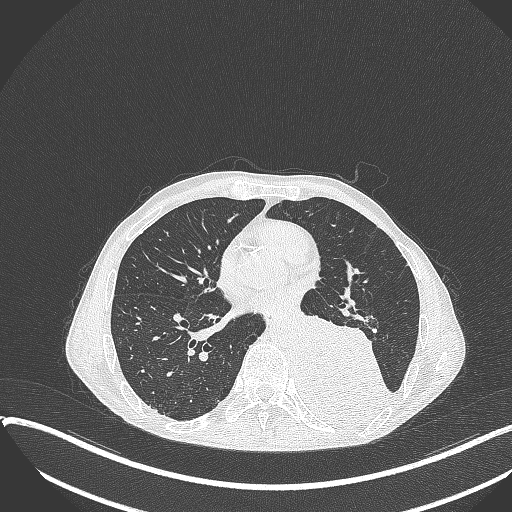
Chest CT, one axial slice. Position 161 of 401 along the scan axis. Reconstruction kernel B70f. 120 kVp. Lung window (W 1500 / L -600 HU). 1 mm slice thickness. 512 × 512 image matrix. Patient: male, 57 years. From the clinical record (not read from this slice): clinical TNM (as recorded): T4 N0 M0.
Outlined on this slice (bounding box drawn by a radiologist):
- lung tumour (recorded histology: squamous cell carcinoma): bounding box (x1, y1, x2, y2) in pixels: (296, 306, 391, 433)